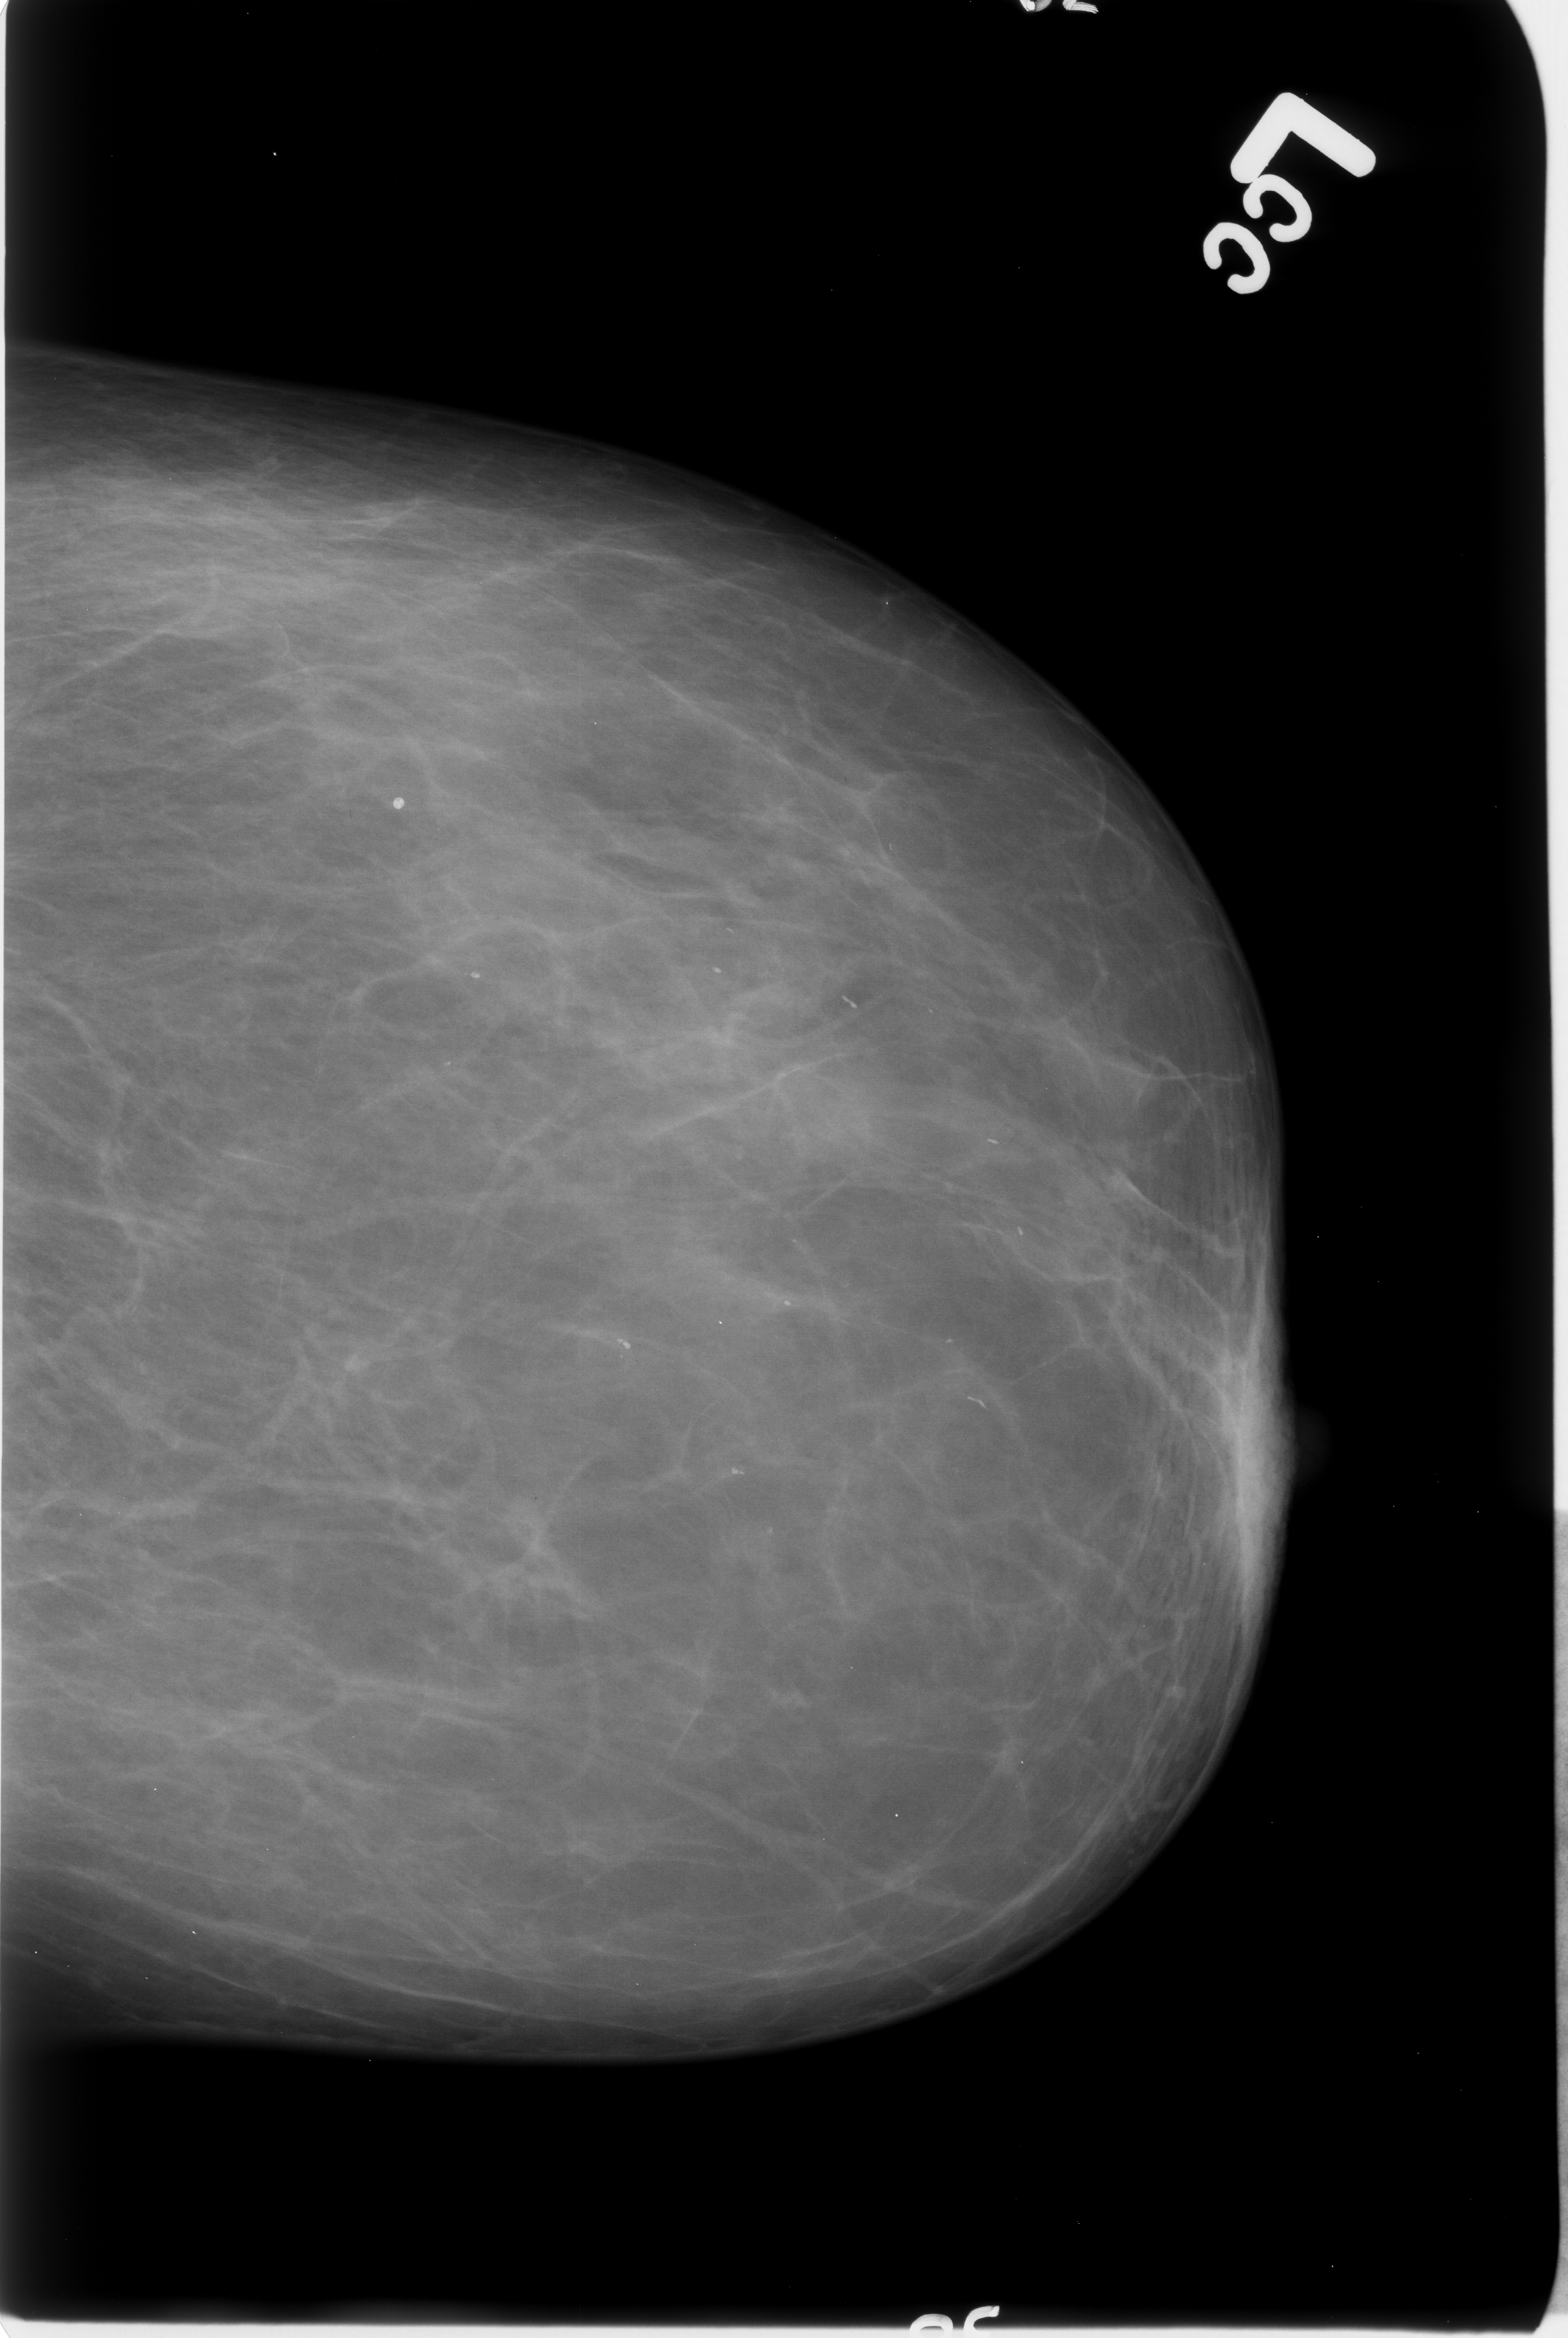
Scanned film-screen mammogram, left breast, craniocaudal (CC) view.
Marked findings (only marked abnormalities are described; nothing is implied about the rest of the image): Finding 1 of 3: calcifications, distribution regional; BI-RADS assessment category 2; benign without callback (not worked up further). Finding 2 of 3: calcifications, distribution regional; BI-RADS assessment category 2; subtlety rating 3 on a 1 (subtle) to 5 (obvious) scale; benign; no additional work-up was recommended (benign without callback). Finding 3 of 3: calcifications, distribution regional; BI-RADS assessment category 2; subtlety rating 3 on a 1 (subtle) to 5 (obvious) scale; benign without callback (not worked up further).